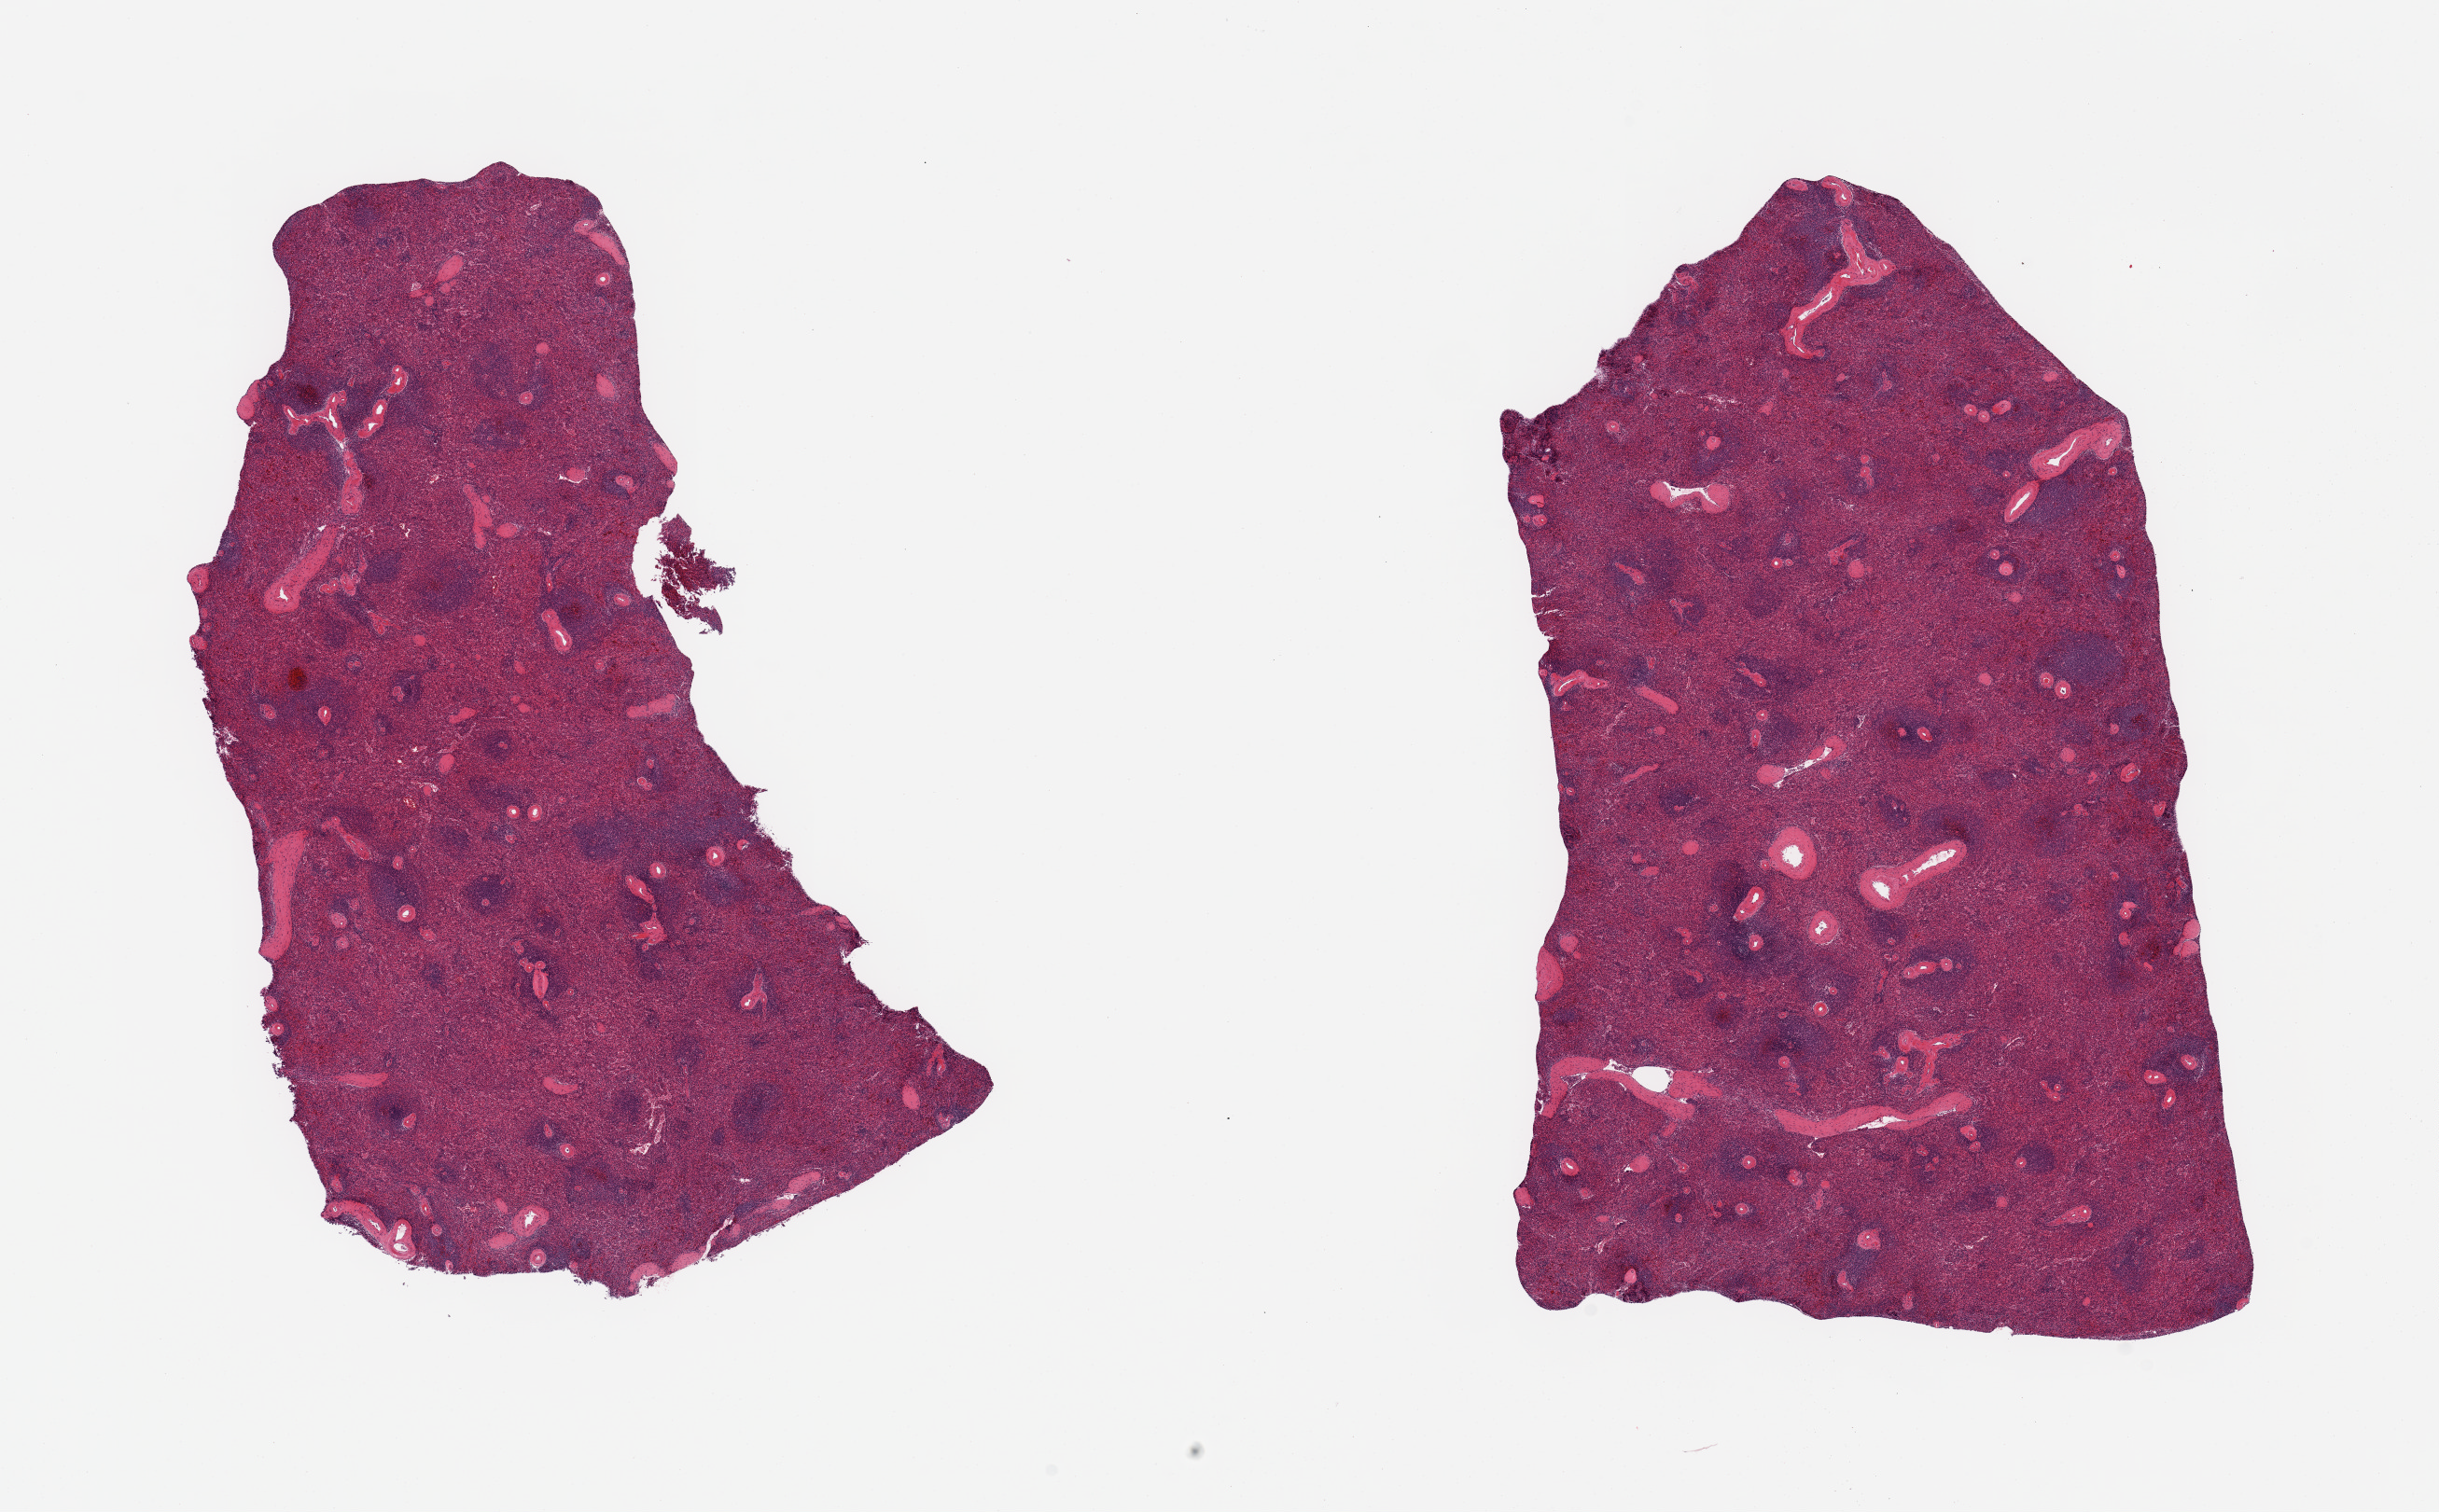
H&E whole-slide image, brightfield, shown as a low-resolution overview of the whole scanned area (about 20.7 x 12.8 mm), PAXgene-fixed paraffin-embedded (PFPE) section, section of spleen (target tissue), tissue donor sample. Donor sex: male.
Reviewer comment on this tissue sample: 2 pieces; minimal congestion.